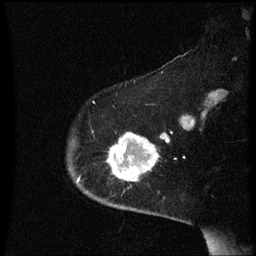
Breast MRI (dynamic contrast-enhanced), one sagittal slice; slice 47 of 60 in the series (ordered by position); dynamic contrast-enhanced series, image 2 of 3 at this slice position (ordered by acquisition); 1.5 T; TE 4.2 ms, TR 8.4 ms; 2 mm slice thickness; 256 × 256 image matrix, field of view 200 × 200 mm. Female patient, age 54 years. From the clinical record (not read from this slice): setting: breast cancer imaged before/during neoadjuvant chemotherapy; receptor status: HR-positive, HER2-negative.
Annotated regions visible in this slice (semi-automatically segmented with operator editing):
- analysis volume of interest (the breast-tissue region the enhancement analysis was run in; not a lesion): bounding box [x1, y1, x2, y2] px = [108, 134, 170, 191]
- tumour enhancement mask (voxels above the 70 % enhancement threshold inside the analysis volume of interest): [108, 134, 170, 181]